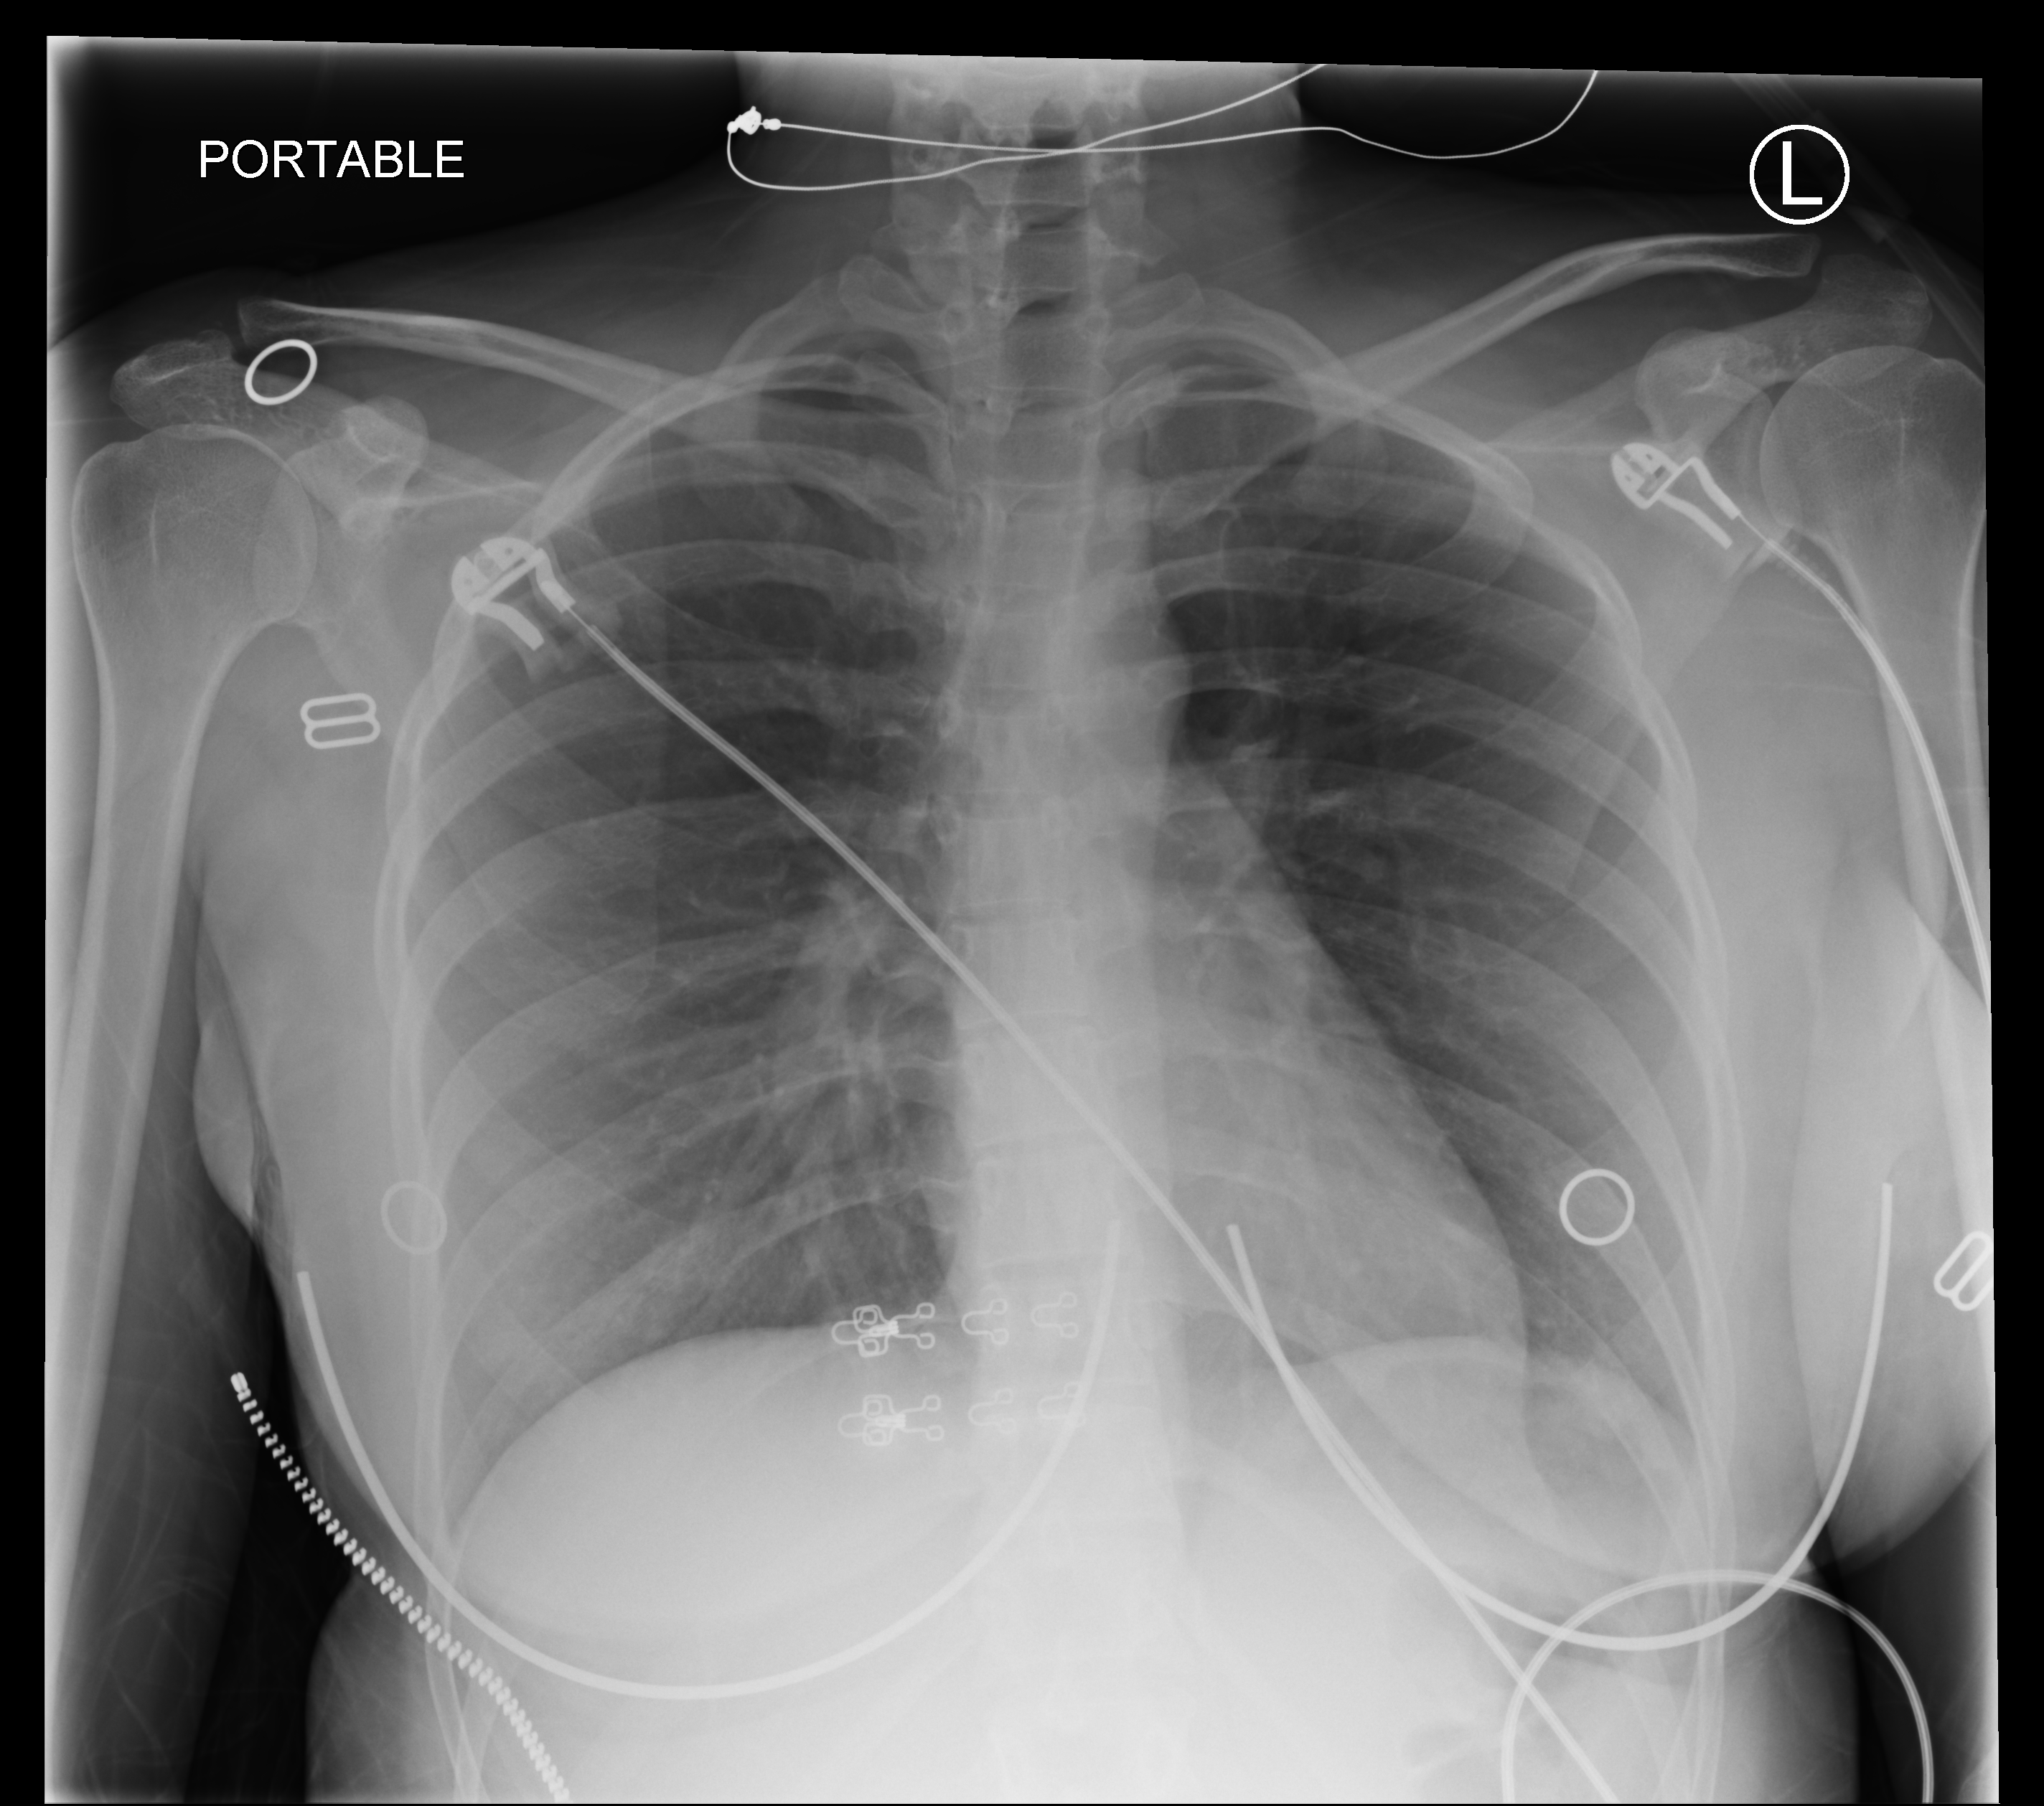
Chest X-ray (portable), anteroposterior (AP) projection. Female patient hospitalised with COVID-19, age 18–59 years.
Hospital-stay facts (about this admission, not read from this image; timing relative to this image not recorded): length of hospital stay: 1 day; admitted to intensive care during this hospital stay: no.